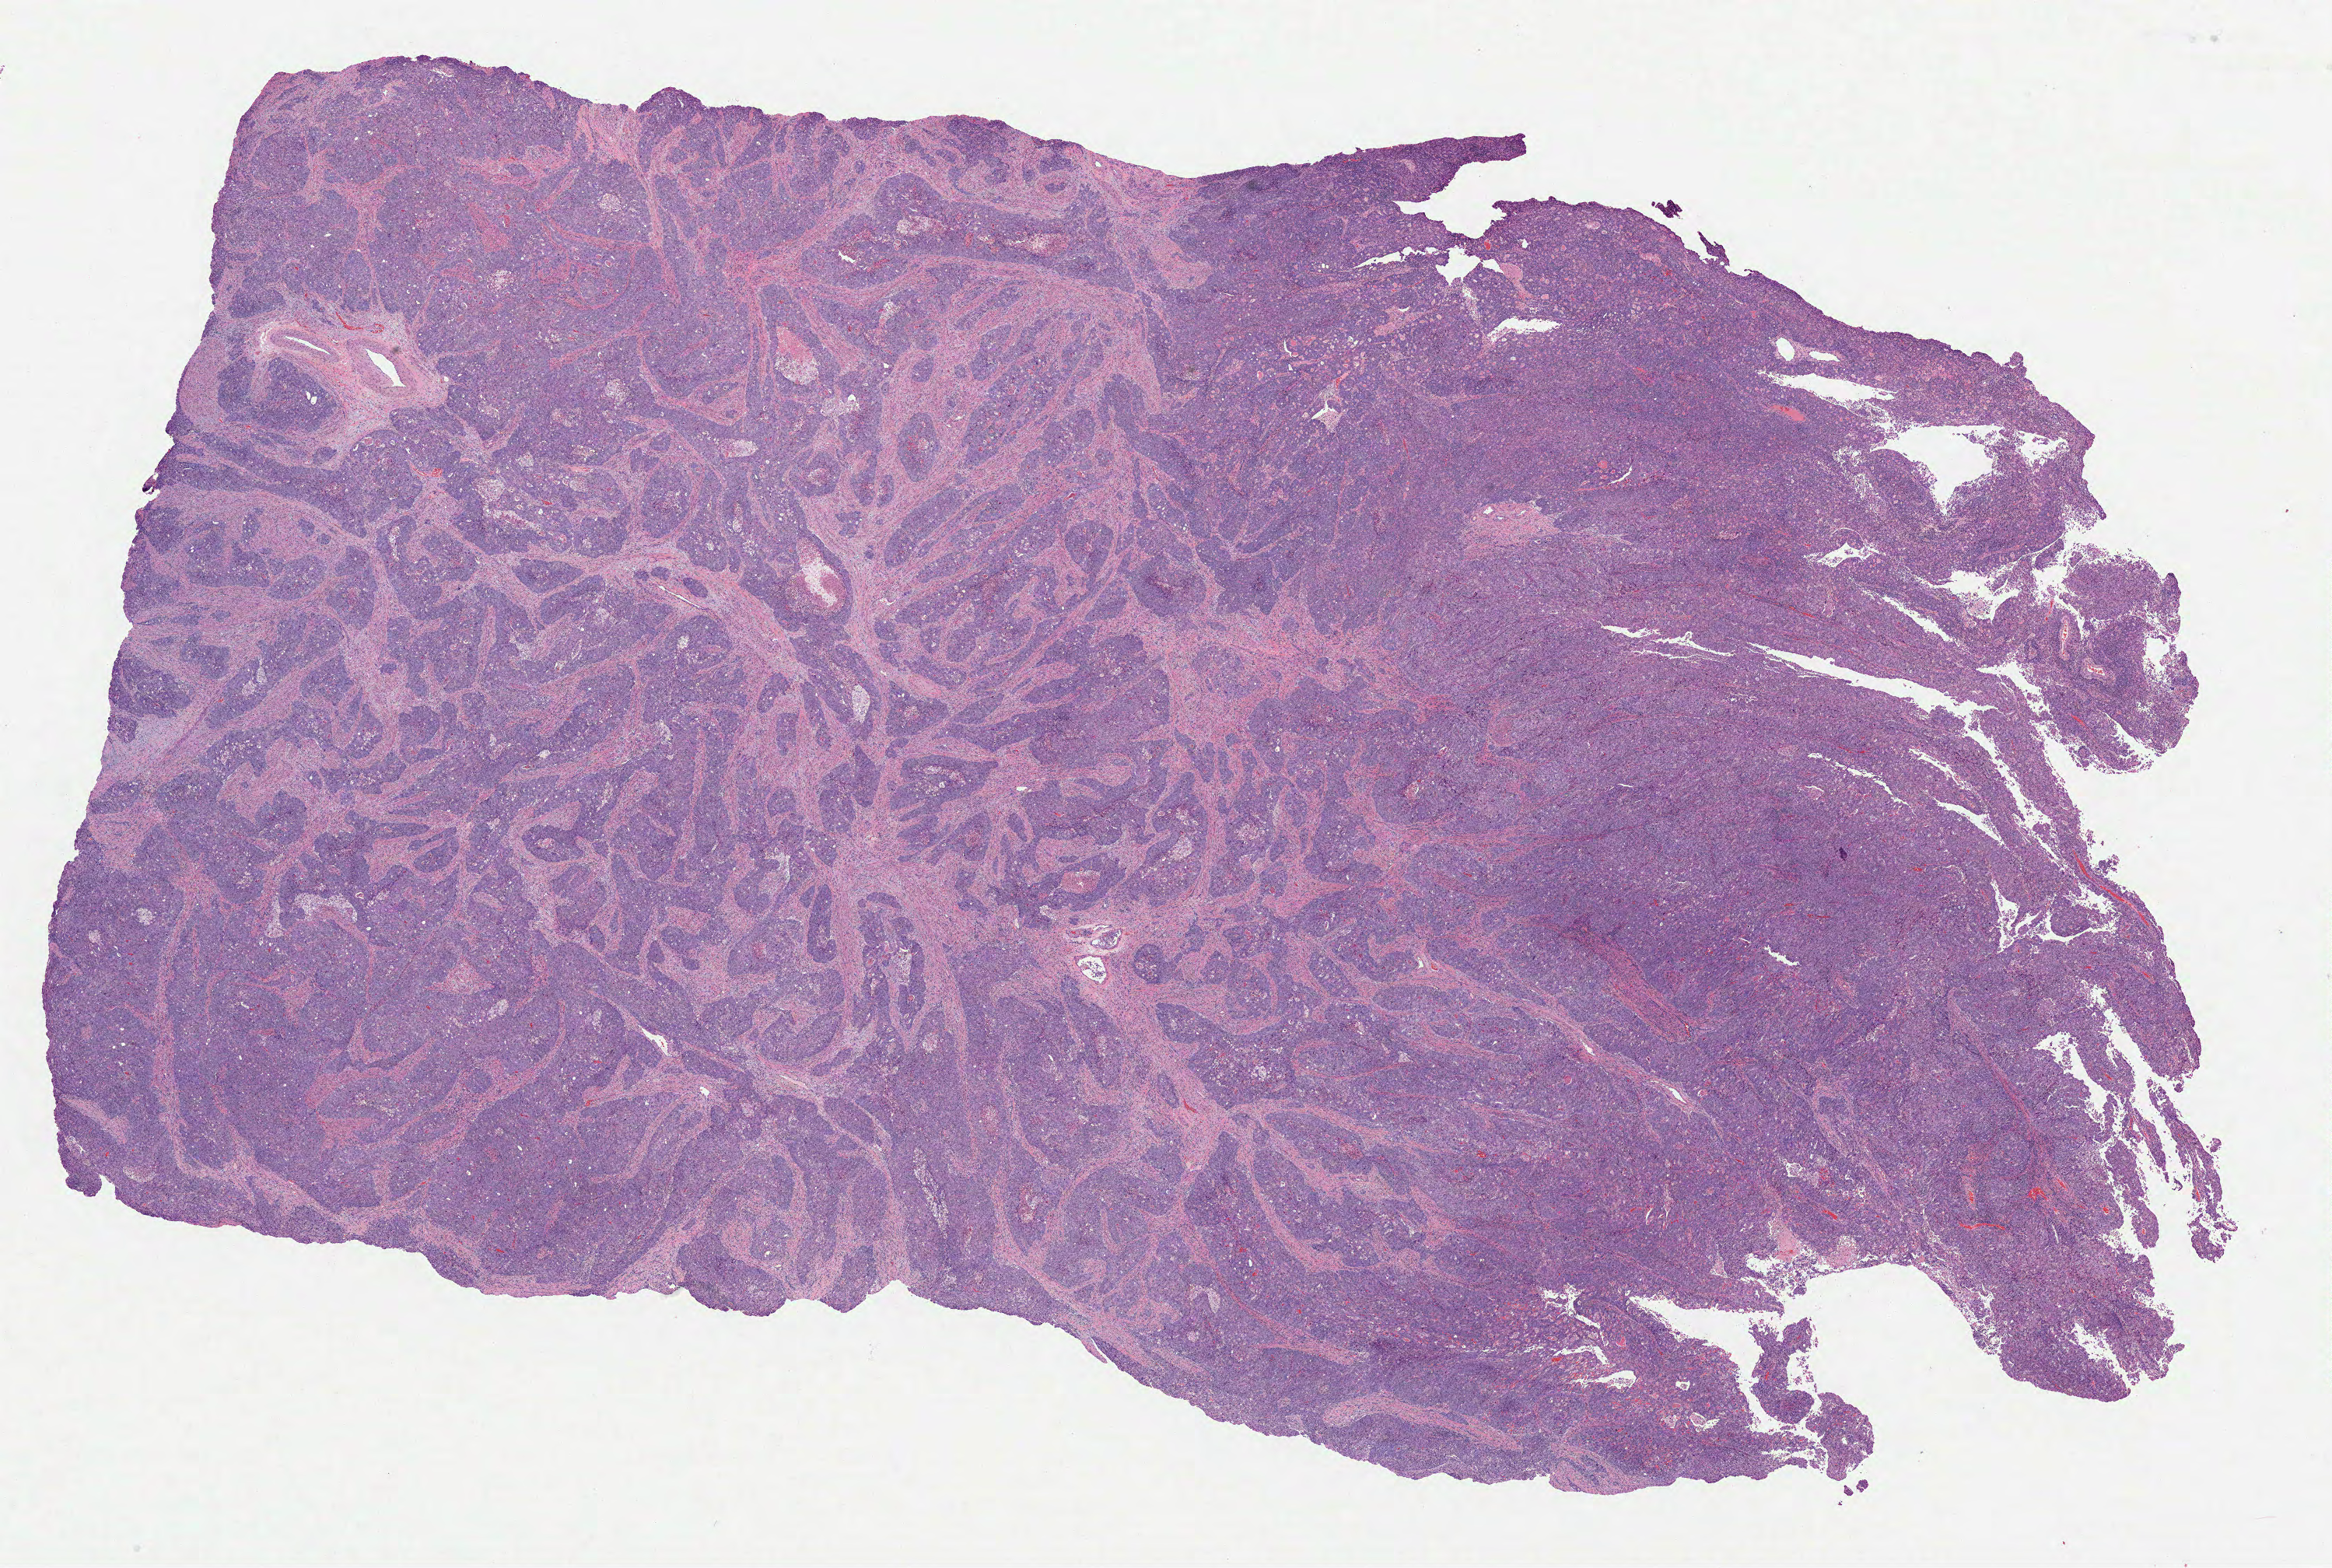
Whole-slide histology image, Hematoxylin and eosin (H&E) stained — whole scanned area (about 24.0 x 16.1 mm, acquisition: 20x scan) shown as a low-resolution overview, formalin-fixed paraffin-embedded (FFPE) diagnostic section, sample: primary tumour, uterus. Female patient; age at initial diagnosis 60 years. Histologic grade: G3 (poorly differentiated).
- FIGO stage: IIIC
- histologic diagnosis: Endometrioid adenocarcinoma, NOS (endometrium)